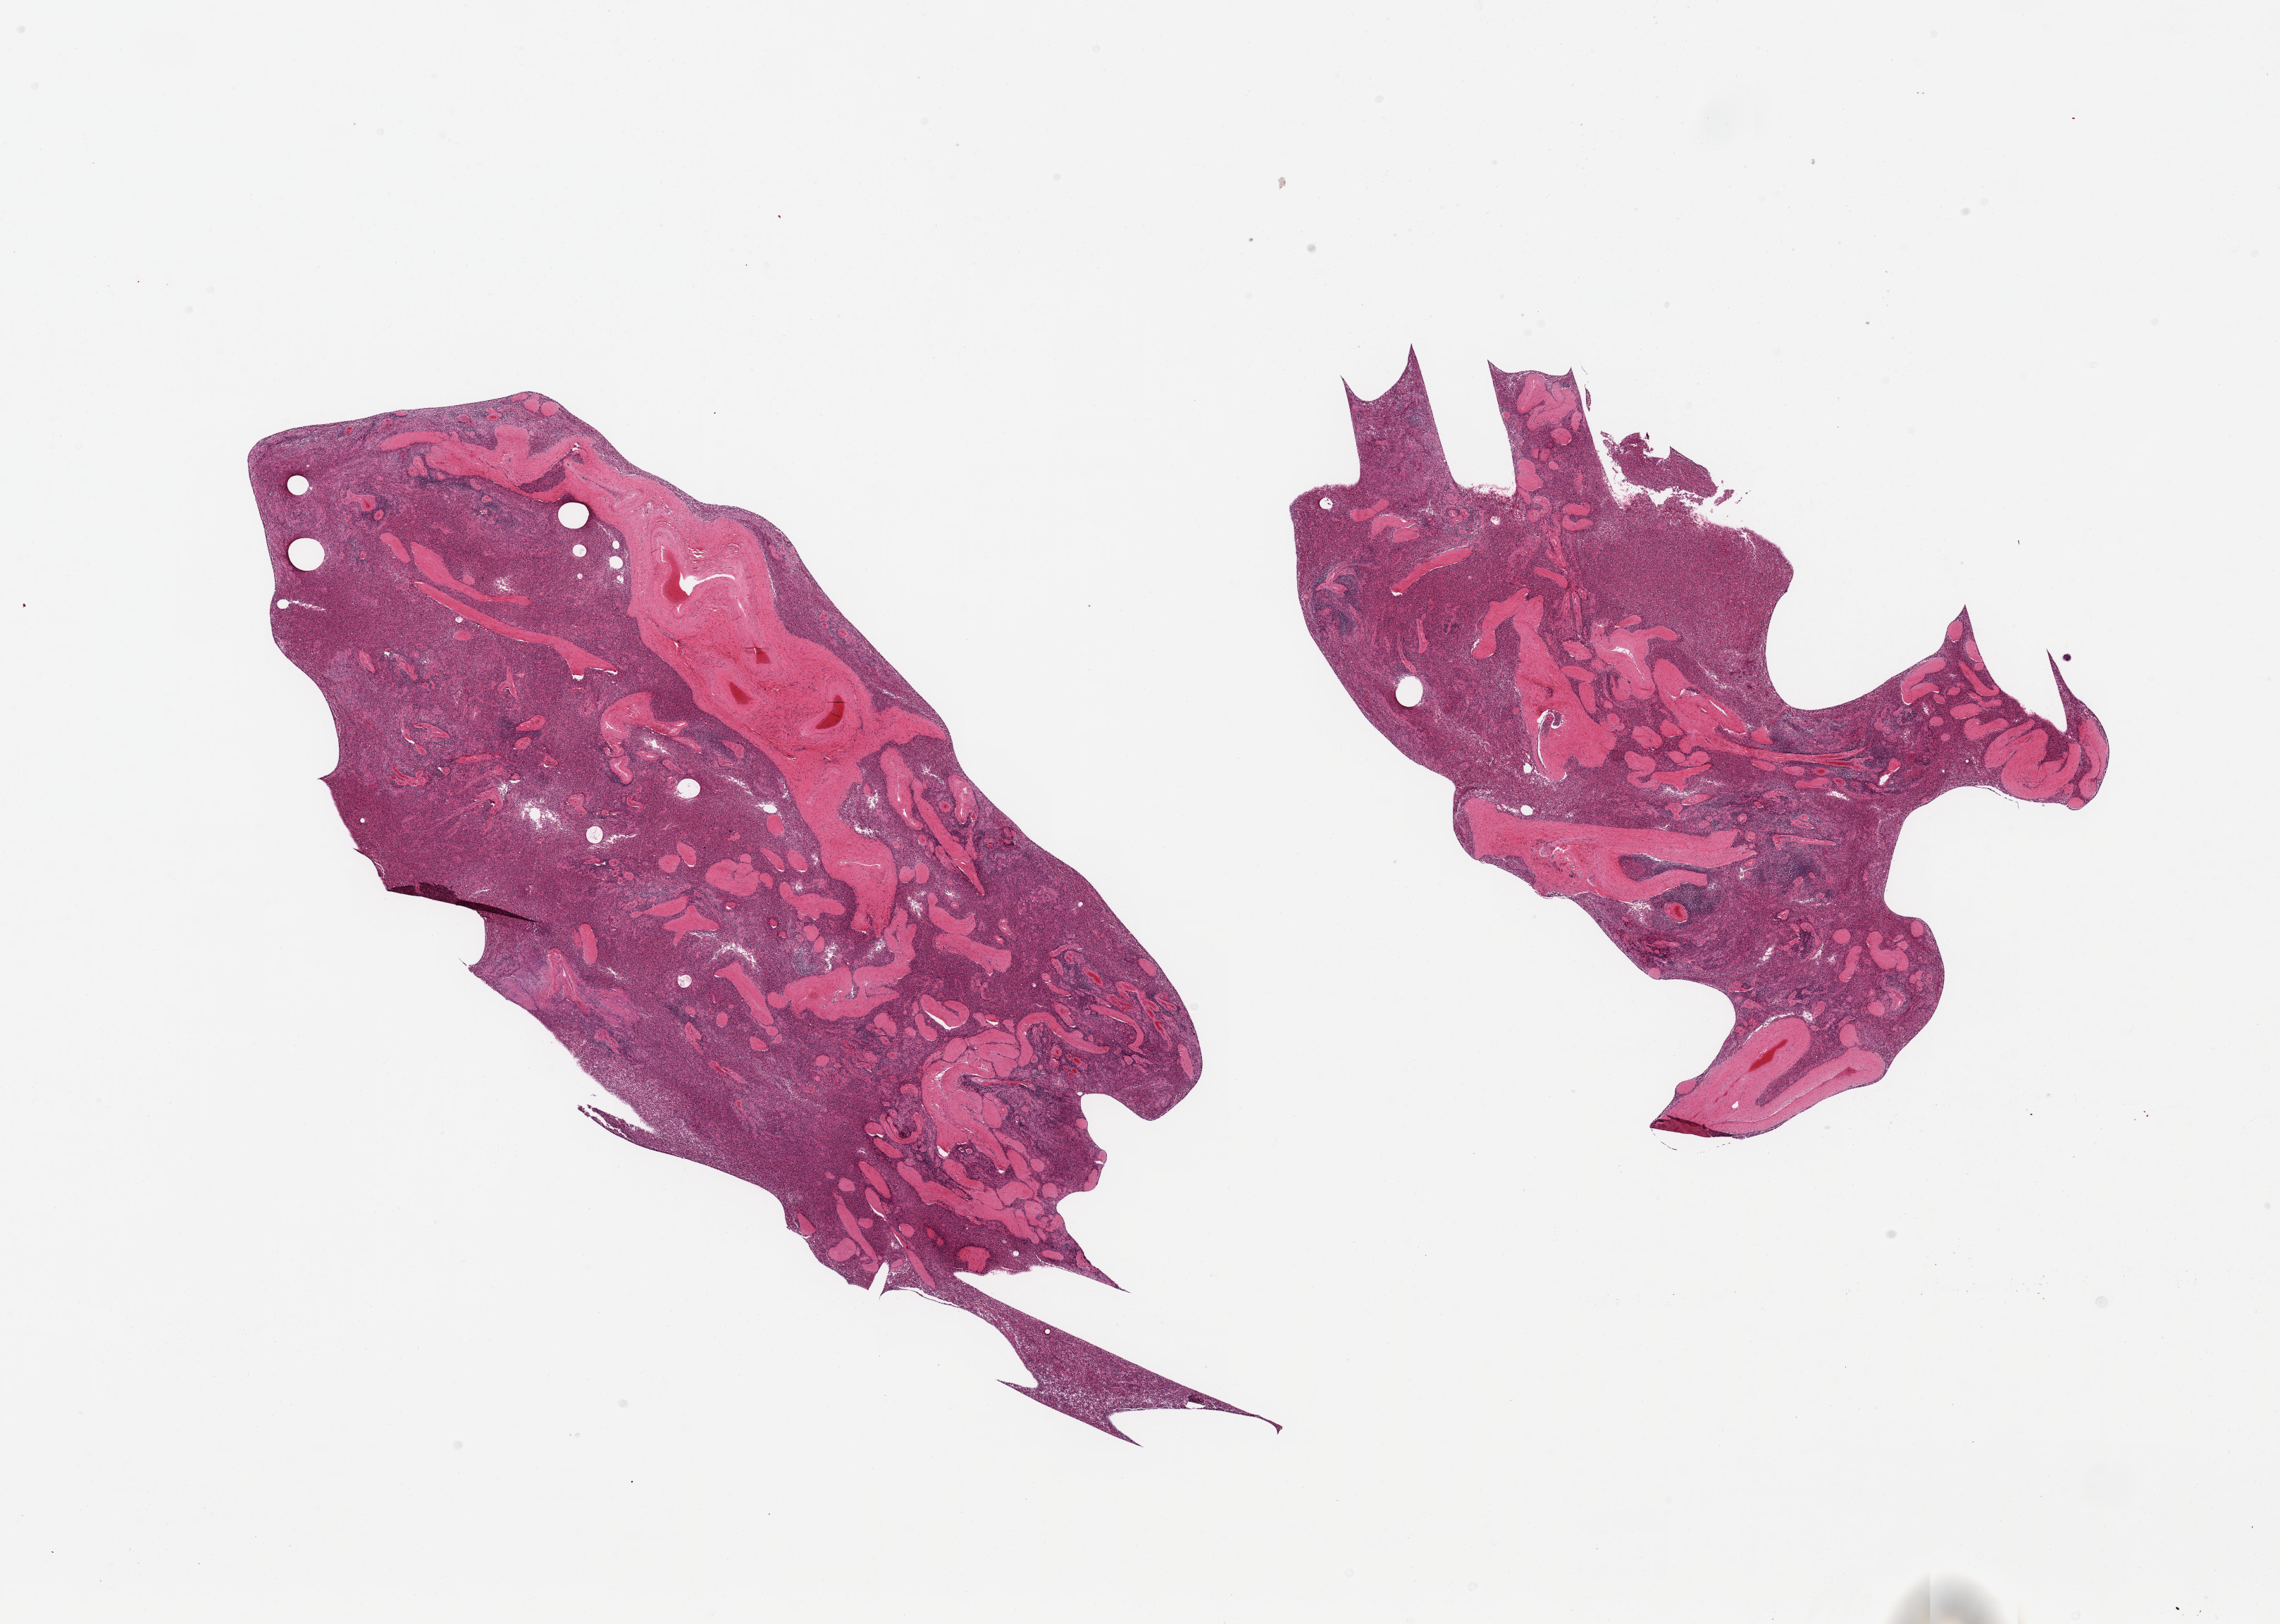
Digitized hematoxylin and eosin (H&E)-stained section — whole scanned area (about 25.6 x 18.2 mm, slide scanned at 20x) shown as a low-resolution overview; PAXgene-fixed paraffin-embedded (PFPE) section; target tissue: spleen; tissue donor sample. Donor: male.
- pathologist's review note for this sample: 2 pieces, moderate congestion; remote splenitis